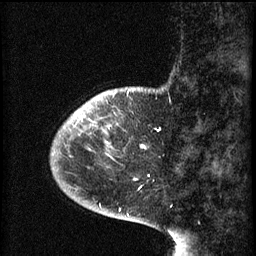
Breast MRI (dynamic contrast-enhanced), one sagittal slice; position 10 of 60 along the scan axis; 3 images stored at this slice position (order not interpretable as contrast timing); 1.5 T; TE 4.2 ms, TR 8.1 ms; 2 mm slice thickness; 256 × 256 image matrix, field of view 200 × 200 mm. Female patient, age 44 years.
Annotated regions visible in this slice (semi-automatically segmented with operator editing):
- analysis volume of interest (the breast-tissue region the enhancement analysis was run in; not a lesion): bounding box [x1, y1, x2, y2] px = [59, 110, 114, 161]
- tumour enhancement mask (voxels above the 70 % enhancement threshold inside the analysis volume of interest): [74, 110, 89, 121]